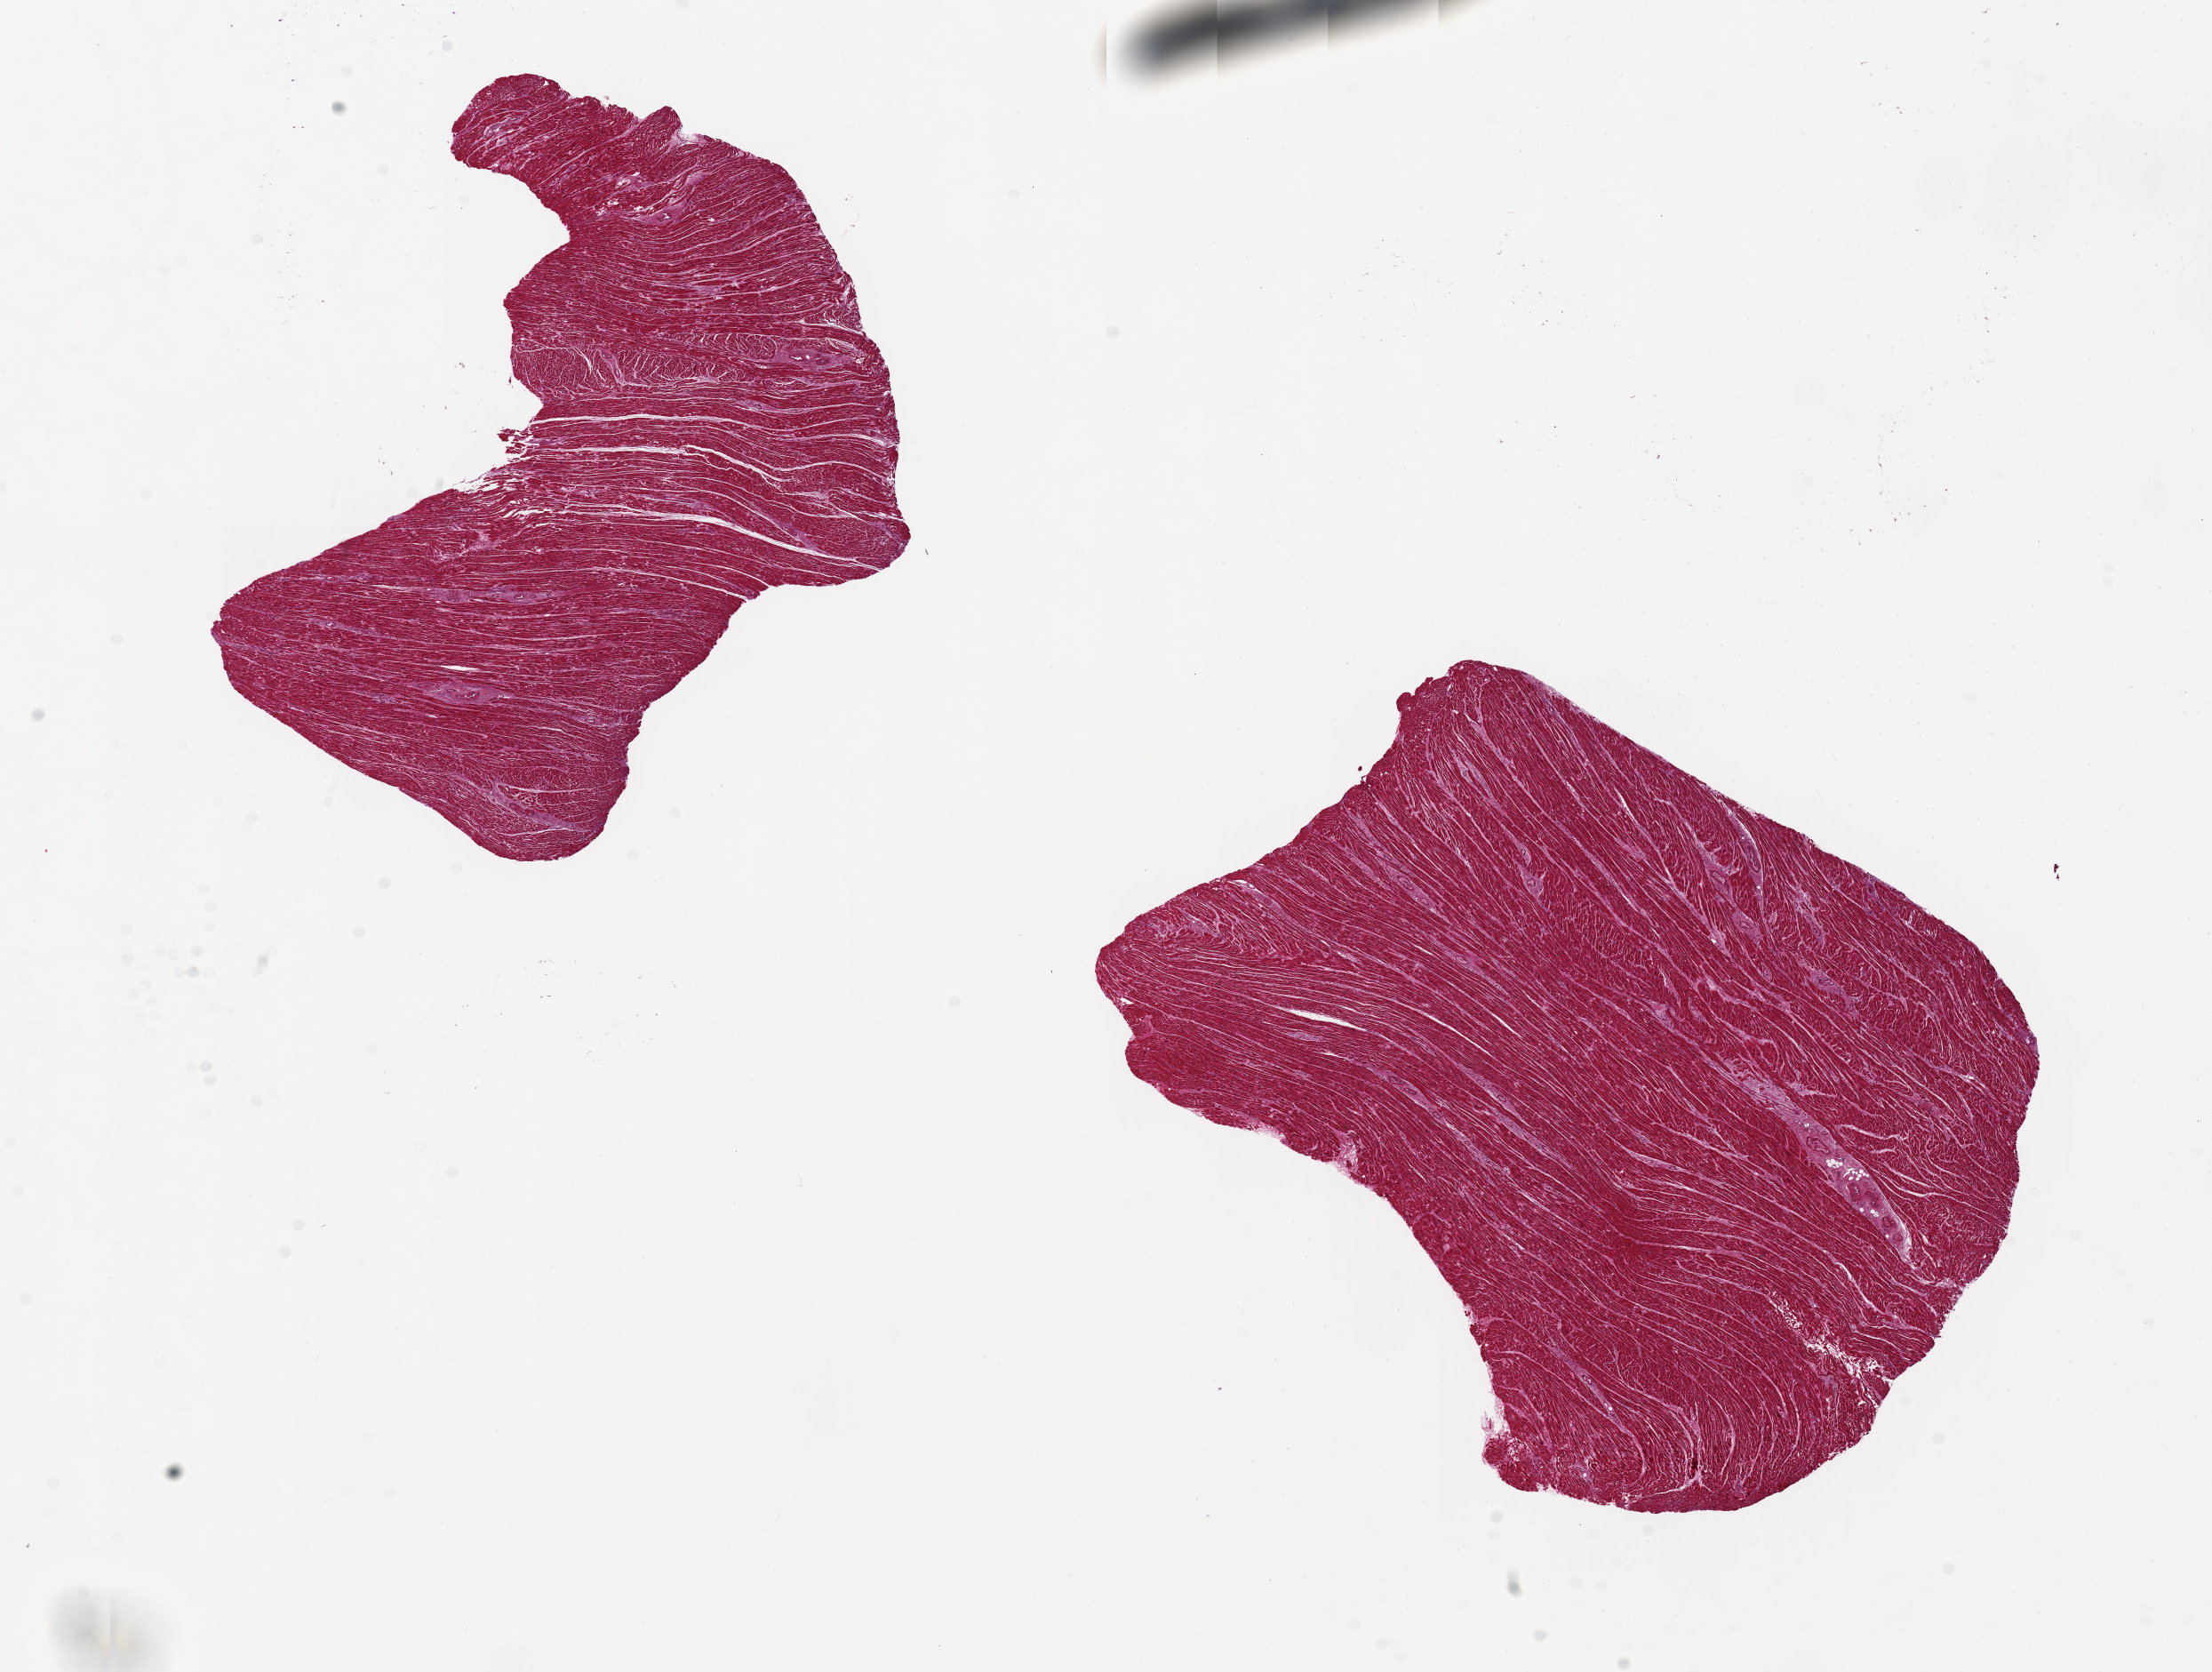
Whole-slide image, haematoxylin and eosin stain, brightfield, low-resolution overview of the scanned area, about 19.7 x 14.9 mm (acquisition: 20x scan). PAXgene-fixed, paraffin-embedded tissue. Target tissue: heart. Tissue donor sample.
* reviewer comment on this tissue sample: 2 pieces ~6x4 mm. Focal ischemic changes (contration bands)